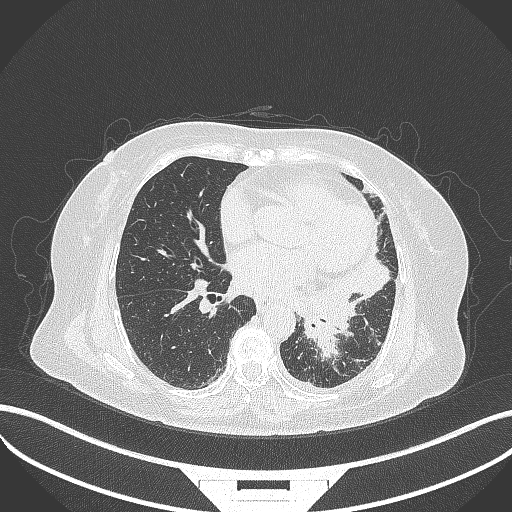
Chest CT, one axial slice; slice 157 of 322 in the series (ordered by position); reconstruction kernel B70f; lung window (W 1500 / L -600 HU); 1 mm slice thickness; 512 × 512 image matrix, field of view 400 × 400 mm. Female patient, age 69 years. Case-level facts recorded for this patient, not image findings: clinical TNM (as recorded): T2b N3 M1.
Outlined on this slice (bounding box drawn by a radiologist):
- lung tumour (recorded histology: adenocarcinoma): bounding box <297,275,356,359> (left, top, right, bottom; pixels)